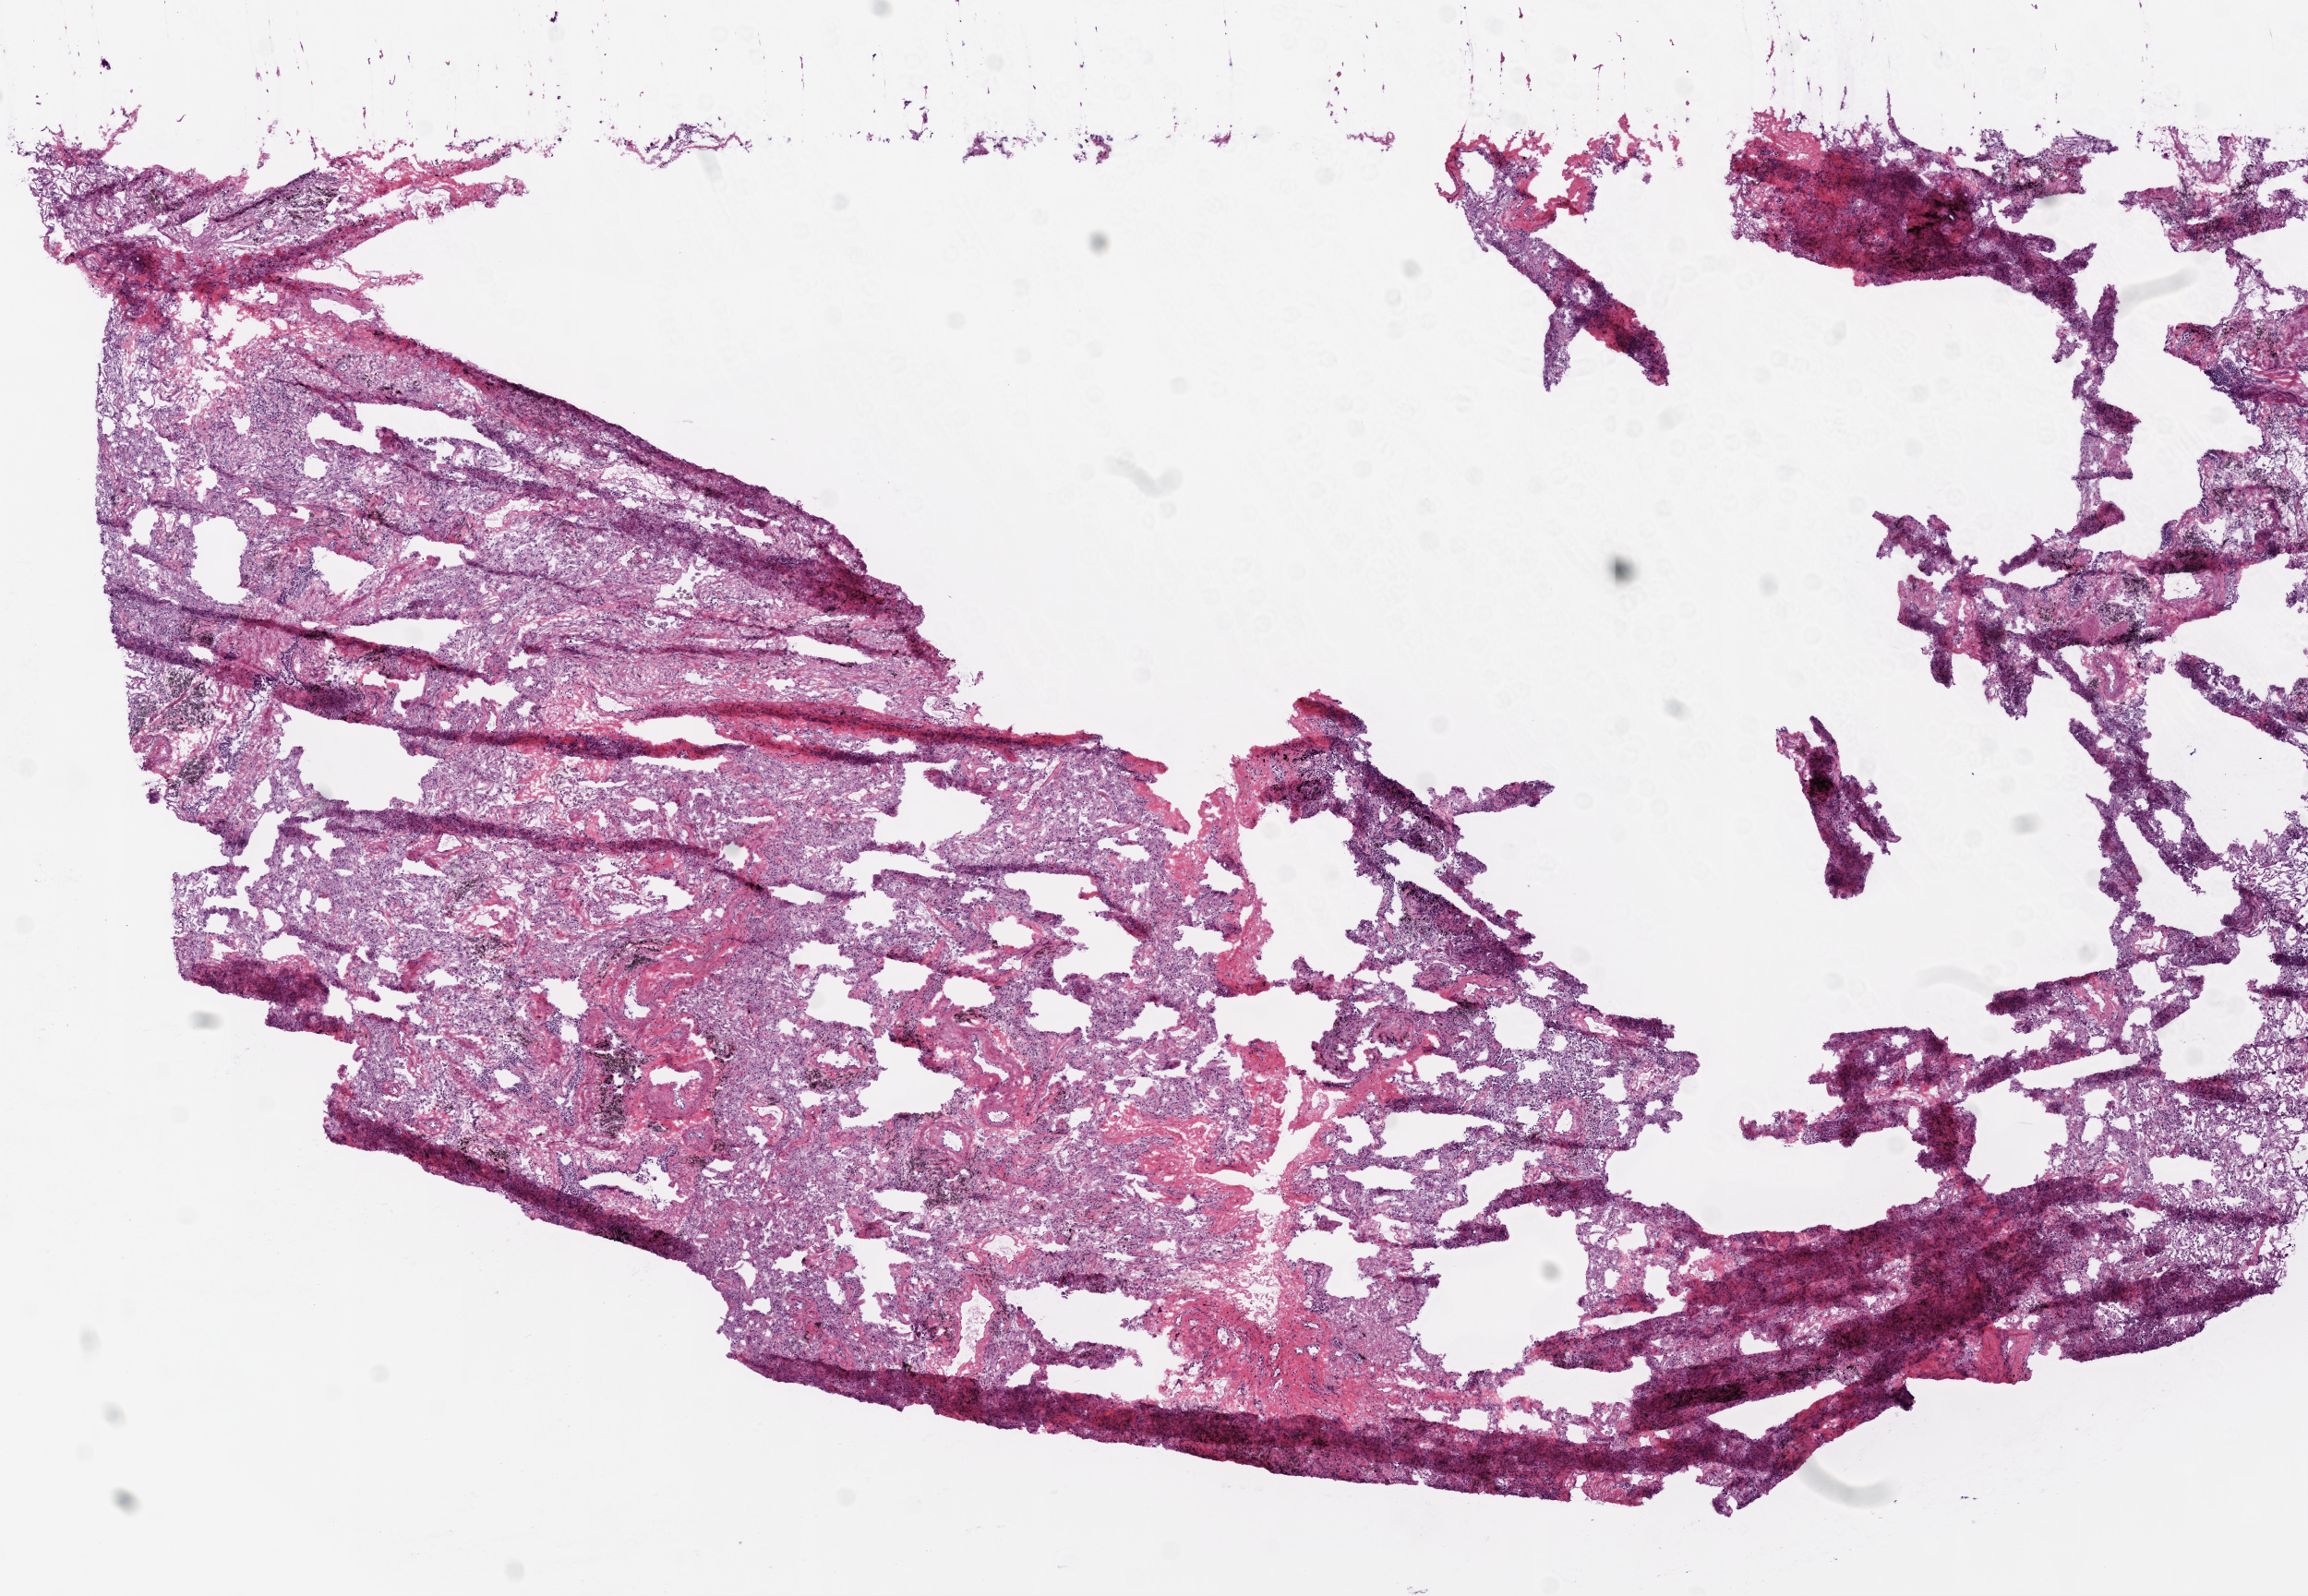
H&E whole-slide image — low-resolution overview of the scanned area, about 10.0 x 6.9 mm (slide scanned at 20x), frozen section from the bottom of the tissue portion, solid tissue normal (non-tumour tissue) sample from the lung. Patient: male, age at initial diagnosis 65 years.
This section: solid tissue normal (non-tumour) sample from the same patient. Patient diagnosis: Squamous cell carcinoma, NOS (upper lobe, lung).